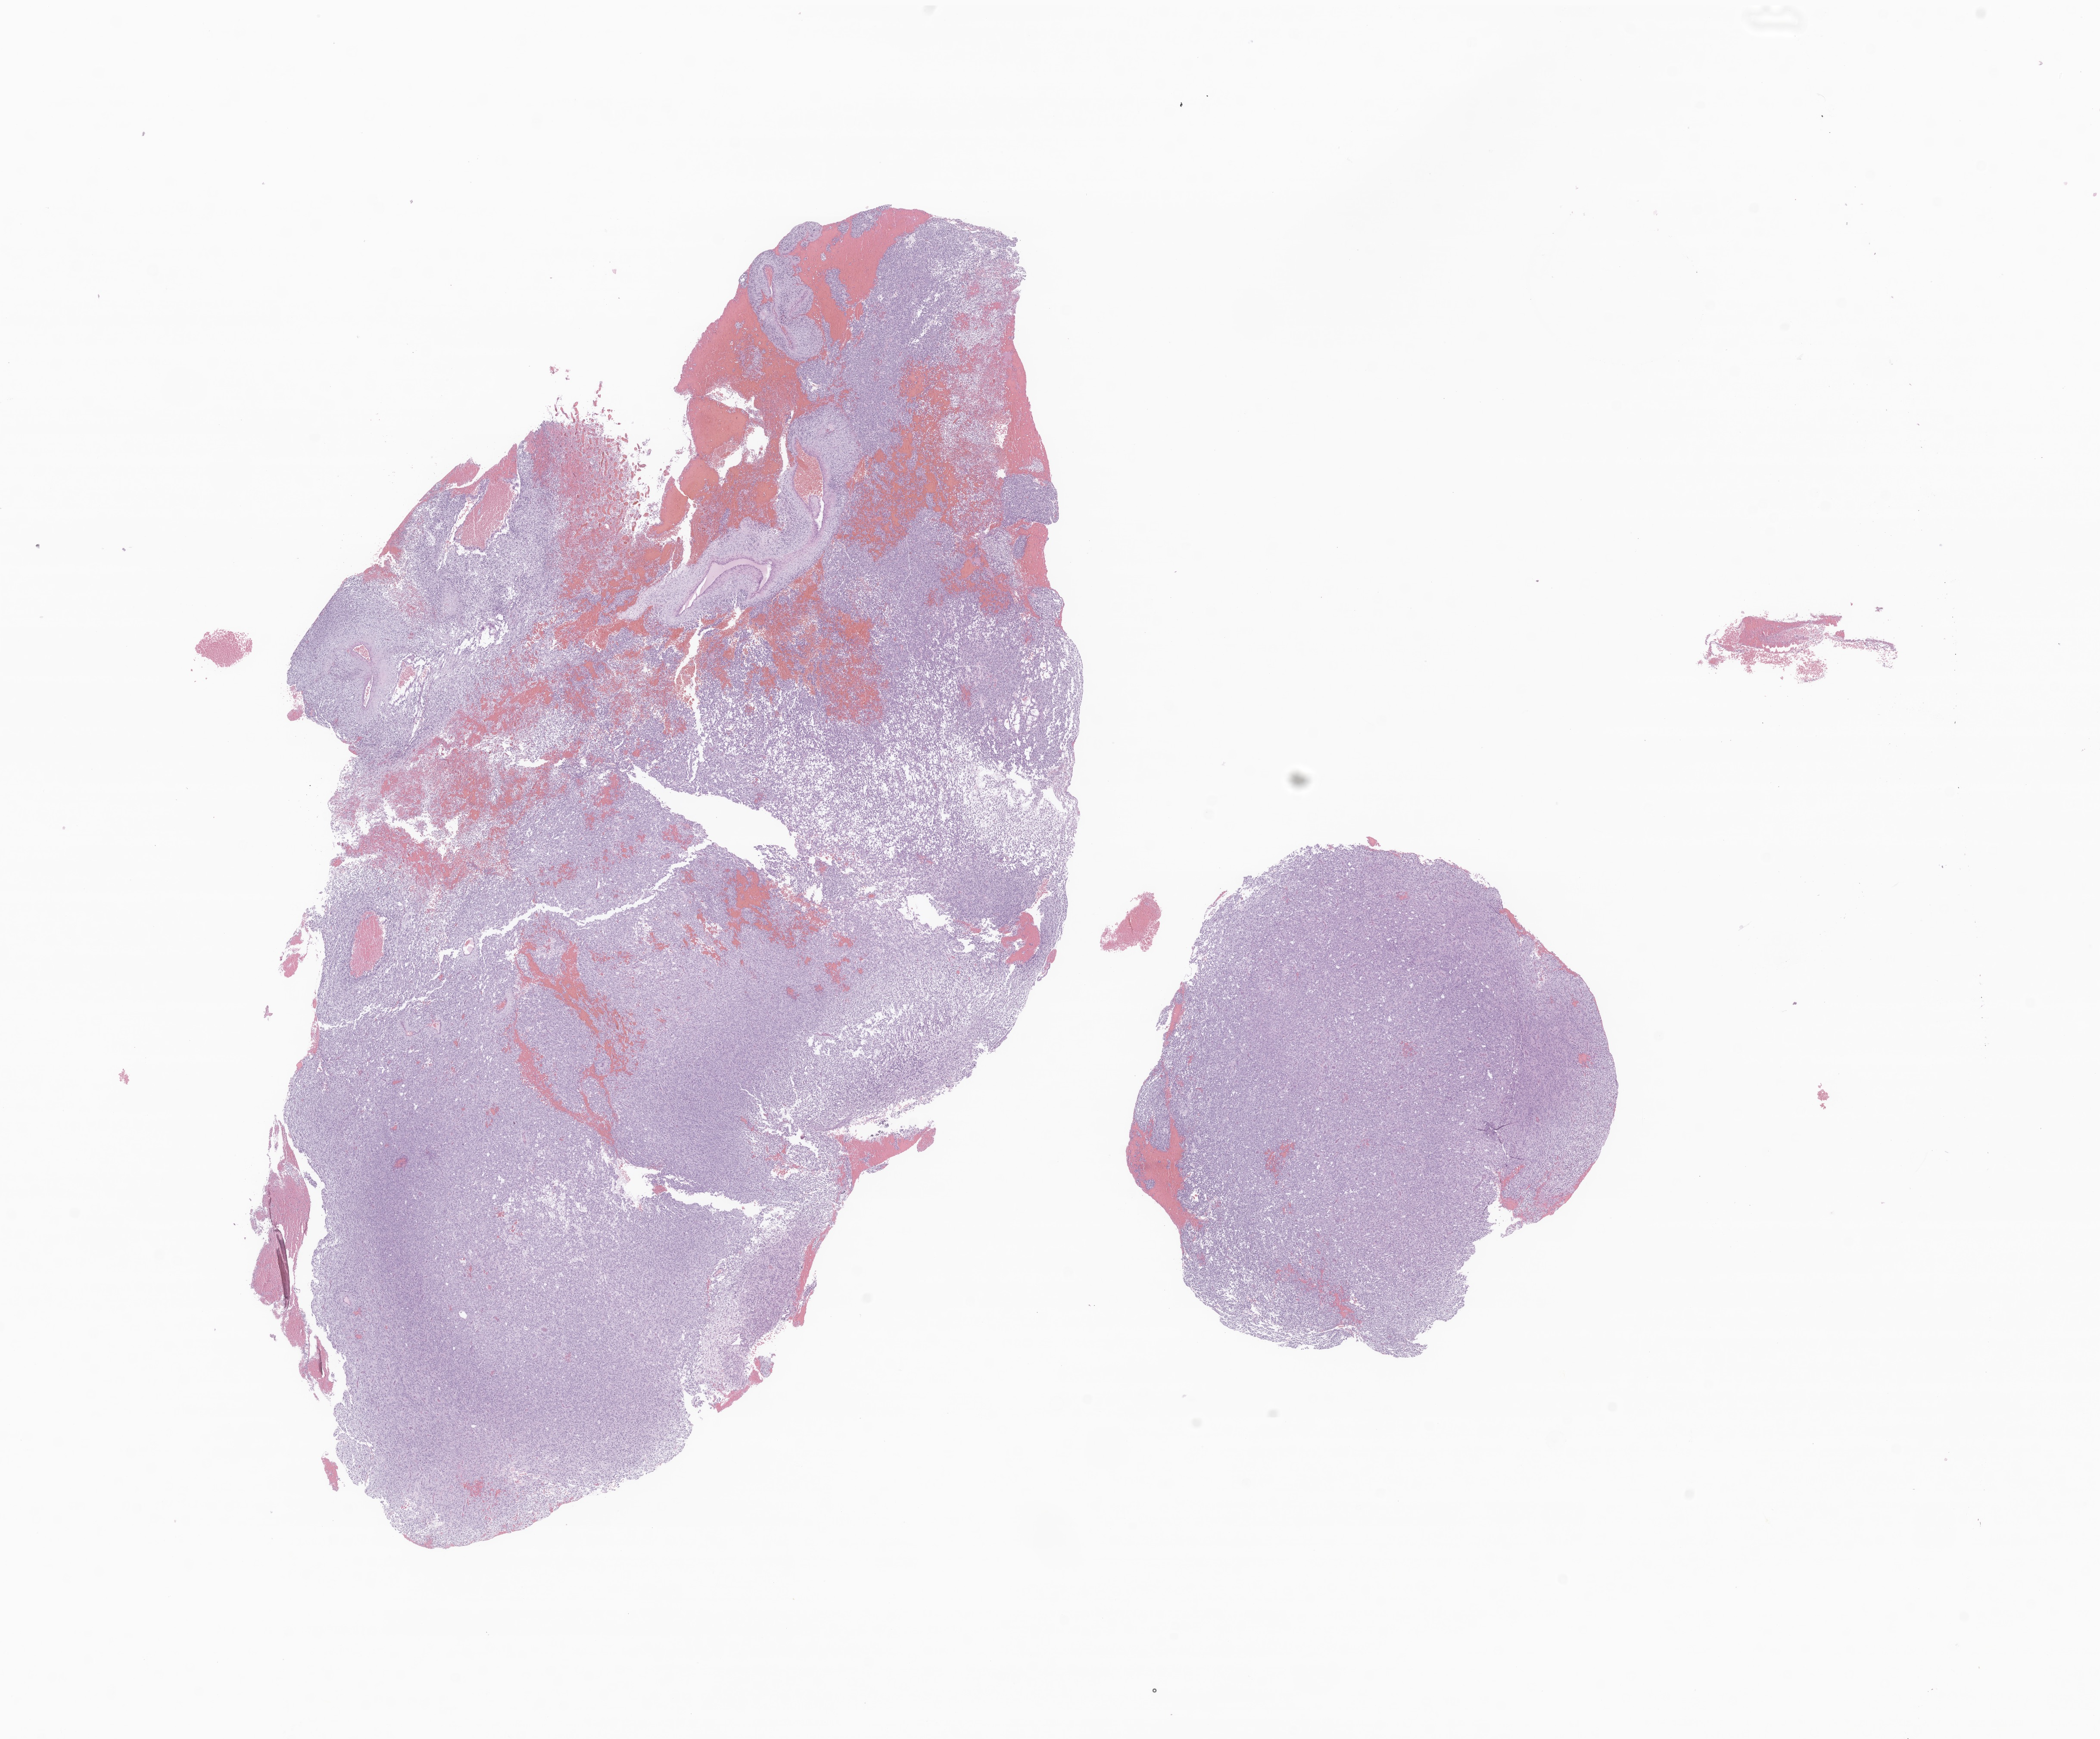
Digitized haematoxylin and eosin-stained section of tumor tissue from the brain — low-resolution overview of the scanned area, about 20.5 x 17.0 mm. Formalin-fixed, paraffin-embedded (FFPE) tissue. Patient: male, age 45 months (3 years 9 months).
Diagnosis: Neoplasm, malignant.